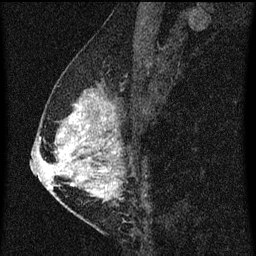
Breast MRI (dynamic contrast-enhanced), one sagittal slice. Position 26 of 60 along the scan axis. Dynamic contrast-enhanced series, image 2 of 3 at this slice position (ordered by acquisition). 1.5 T. TE 4.2 ms, TR 8 ms. 2 mm slice thickness. 256 × 256 image matrix, field of view 180 × 180 mm. Female patient, age 47 years.
Outlined on this slice (semi-automatic segmentation, software-assisted and operator-edited):
- analysis volume of interest (the breast-tissue region the enhancement analysis was run in; not a lesion): box from (x=50, y=80) to (x=138, y=203) px
- tumour enhancement mask (voxels above the 70 % enhancement threshold inside the analysis volume of interest): (x=51, y=104)–(x=119, y=201)